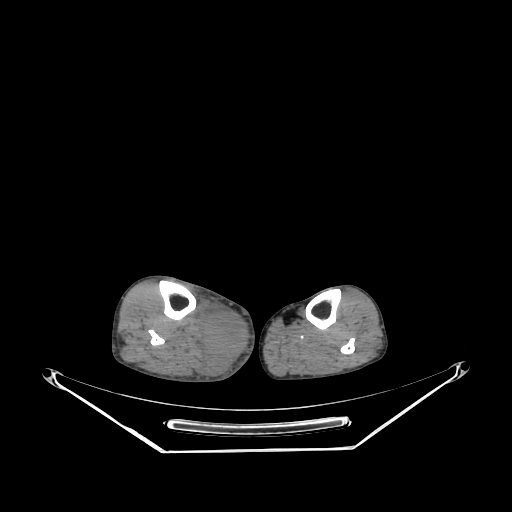
CT of an extremity soft-tissue mass (from a PET/CT study), one axial slice. Slice 130 of 267 in the series (ordered by position). Soft-tissue window (W 400 / L 40 HU). 512 × 512 image matrix, field of view 500 × 500 mm. Male patient. Case-level facts recorded for this patient, not image findings: histological type: pleiomorphic liposarcoma; grade: high; site of the primary tumour: right calf.
Structures marked on this image (expert contour drawn on MRI and transferred to this co-registered scan by the dataset authors):
- gross tumour volume including surrounding oedema: box from (x=199, y=302) to (x=250, y=378) px
- gross tumour volume (mass): (x=203, y=308)–(x=250, y=357)